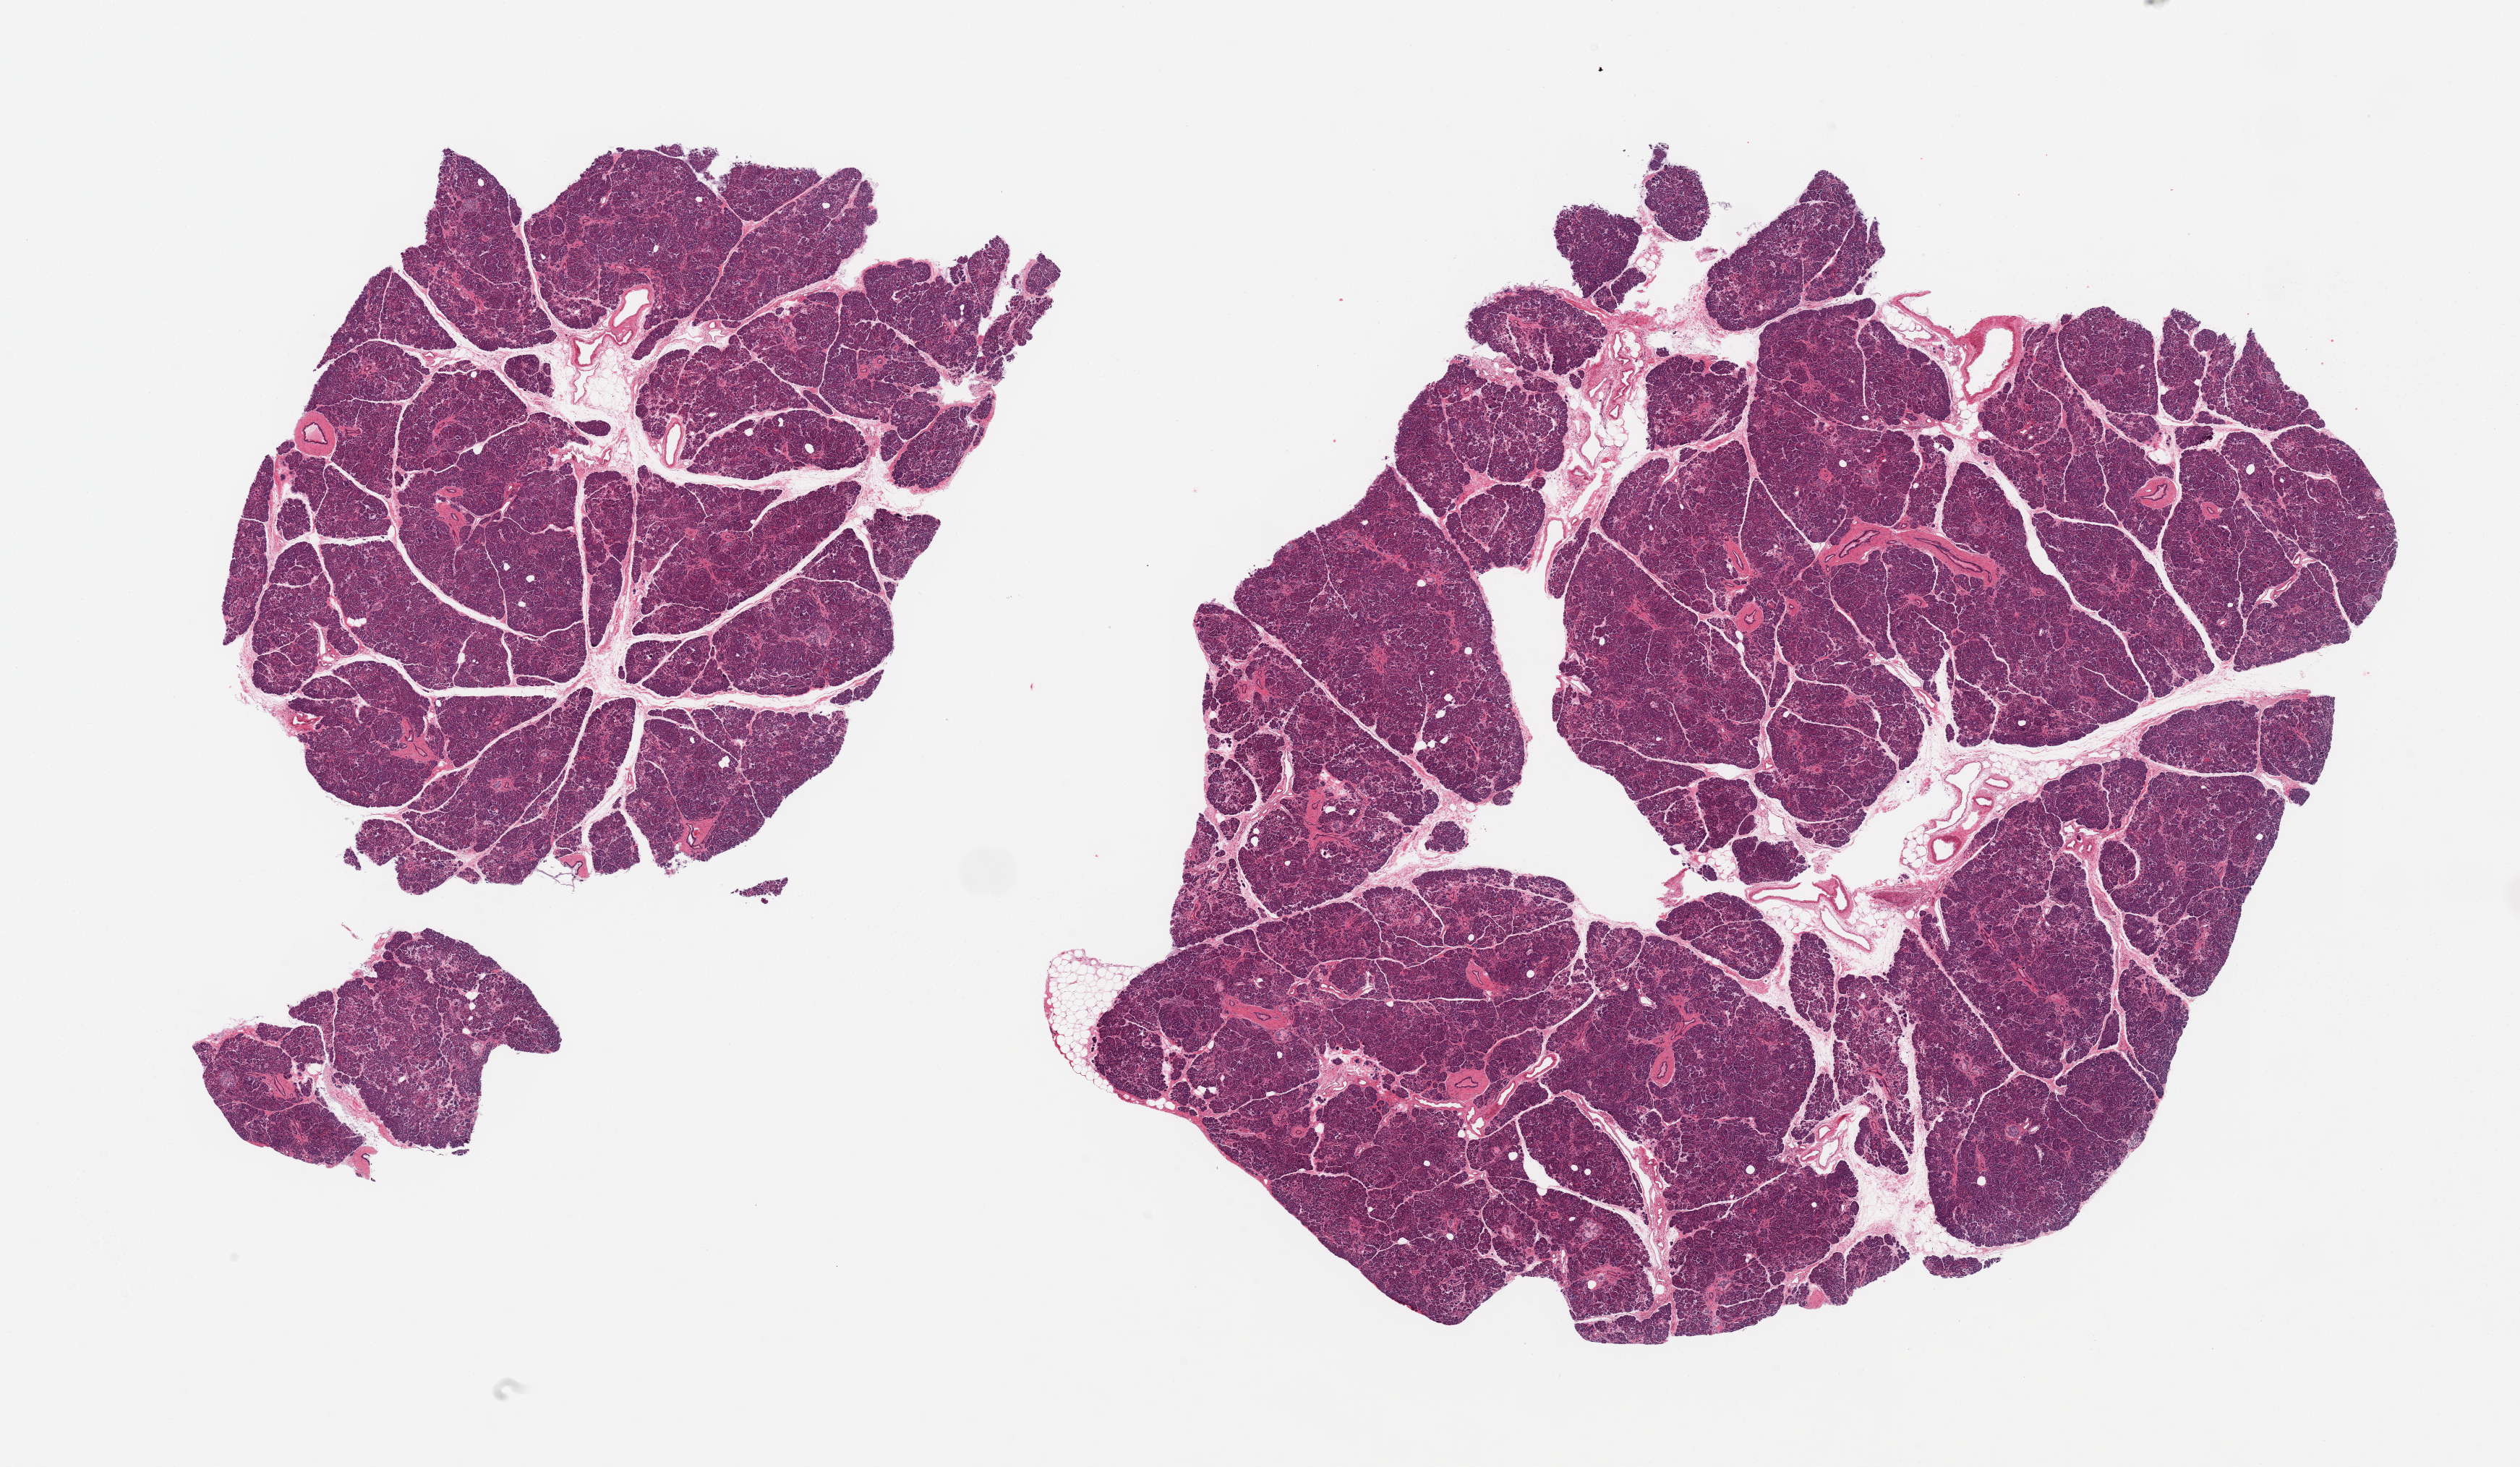
Digitized H&E-stained section, low-resolution overview of the scanned area, about 27.6 x 16.0 mm (acquisition: 20x scan), PAXgene-fixed paraffin-embedded (PFPE) section, target tissue: pancreas, donor tissue sample. Donor sex: male.
Review note (as recorded): 2 pieces; well dissected; no fat; a few partially hyalinized islets.